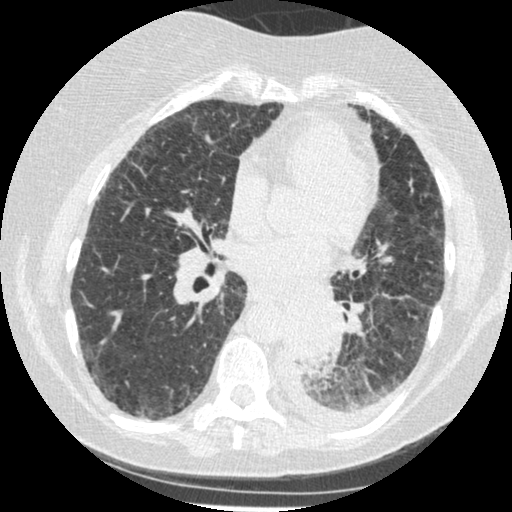
Low-dose screening chest CT, one axial slice; position 108 of 341 along the scan axis; 120 kVp; lung window (W 1500 / L -600 HU); 1.25 mm slice thickness; 512 × 512 image matrix.
Structures marked on this image (expert manual segmentation):
- lesion 1 (tumor, lower lobe of left lung): bounding box <285,302,338,364> (left, top, right, bottom; pixels)